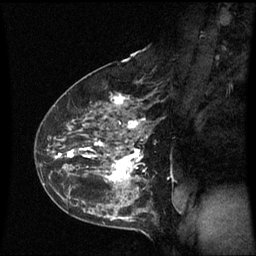
Breast MRI (dynamic contrast-enhanced), one sagittal slice. Slice 38 of 60 in the series (ordered by position). Dynamic contrast-enhanced series, image 2 of 3 at this slice position (ordered by acquisition). 1.5 T. TE 4.2 ms, TR 8.9 ms. 256 × 256 image matrix, field of view 210 × 210 mm. Female patient, age 43 years. Case-level facts recorded for this patient, not image findings: setting: breast cancer imaged before/during neoadjuvant chemotherapy; receptor status: HER2-positive.
Annotated regions visible in this slice (semi-automatic segmentation, software-assisted and operator-edited):
- analysis volume of interest (the breast-tissue region the enhancement analysis was run in; not a lesion): bounding box <56,80,154,195> (left, top, right, bottom; pixels)
- tumour enhancement mask (voxels above the 70 % enhancement threshold inside the analysis volume of interest): <57,95,144,182>